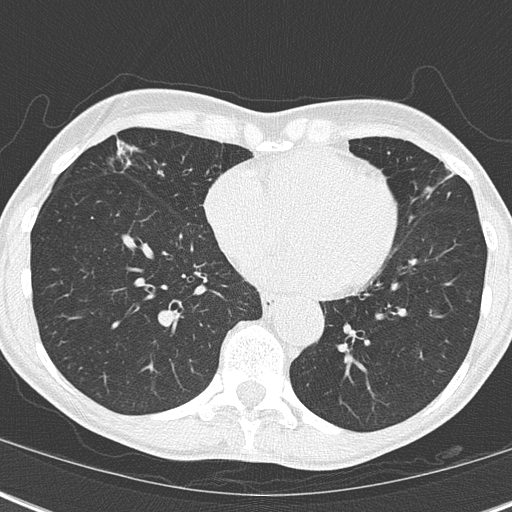
Axial slice from a low-dose chest CT screening exam, third screening round (two years after baseline), lung window (W 1500 / L -600 HU), slice 109 of 173 in the series, 512 × 512 image matrix. Female, age 67 years at enrolment. Current smoker at enrolment.
Expert-annotated lung lesion, bounding box (x1, y1, x2, y2) in pixels: (89, 133, 184, 206). Reader record for this screening exam (exam-level; its link to the box is not recorded): non-calcified nodule or mass ≥4 mm, right middle lobe, 32 × 17 mm, mixed attenuation, pre-existing on the prior screen: yes; interval growth: yes. Participant outcome: lung cancer diagnosed 76 days after this screen — bronchiolo-alveolar adenocarcinoma, NOS, right middle lobe, well differentiated (G1), stage IA (AJCC 6th edition), 25 mm at pathology.